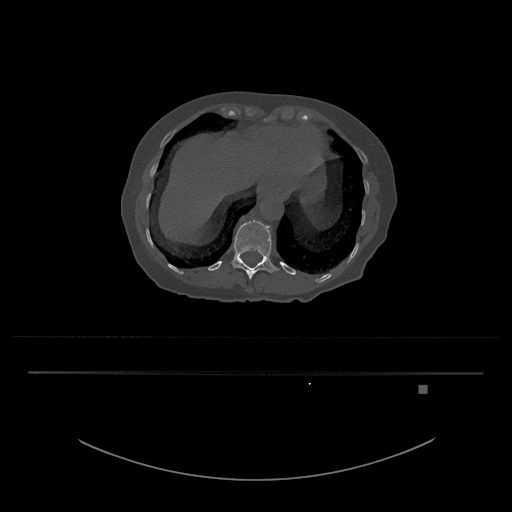
CT including the spine, one axial slice. Slice 613 of 797 in the series (ordered by position). 120 kVp. Bone window (W 1800 / L 400 HU). 512 × 512 image matrix, field of view 500 × 500 mm. Female patient, age 57 years. Case-level facts recorded for this patient, not image findings: primary cancer: cervical.
Outlined on this slice (semi-automatically segmented with operator editing):
- T12 vertebra: bounding box [x1, y1, x2, y2] px = [231, 220, 279, 280]